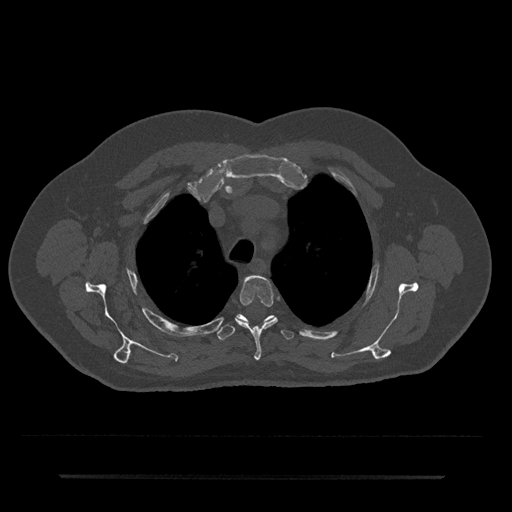
CT including the spine, one axial slice. Slice 556 of 797 in the series (ordered by position). Bone window (W 1800 / L 400 HU). 0.5 mm slice thickness. 512 × 512 image matrix, field of view 437 × 437 mm. Male patient, age 69 years. Case-level facts recorded for this patient, not image findings: primary cancer: prostate.
Outlined on this slice (semi-automatic segmentation, software-assisted and operator-edited):
- T3 vertebra: bounding box (x1, y1, x2, y2) in pixels: (236, 276, 278, 360)
- T4 vertebra: (217, 314, 294, 340)